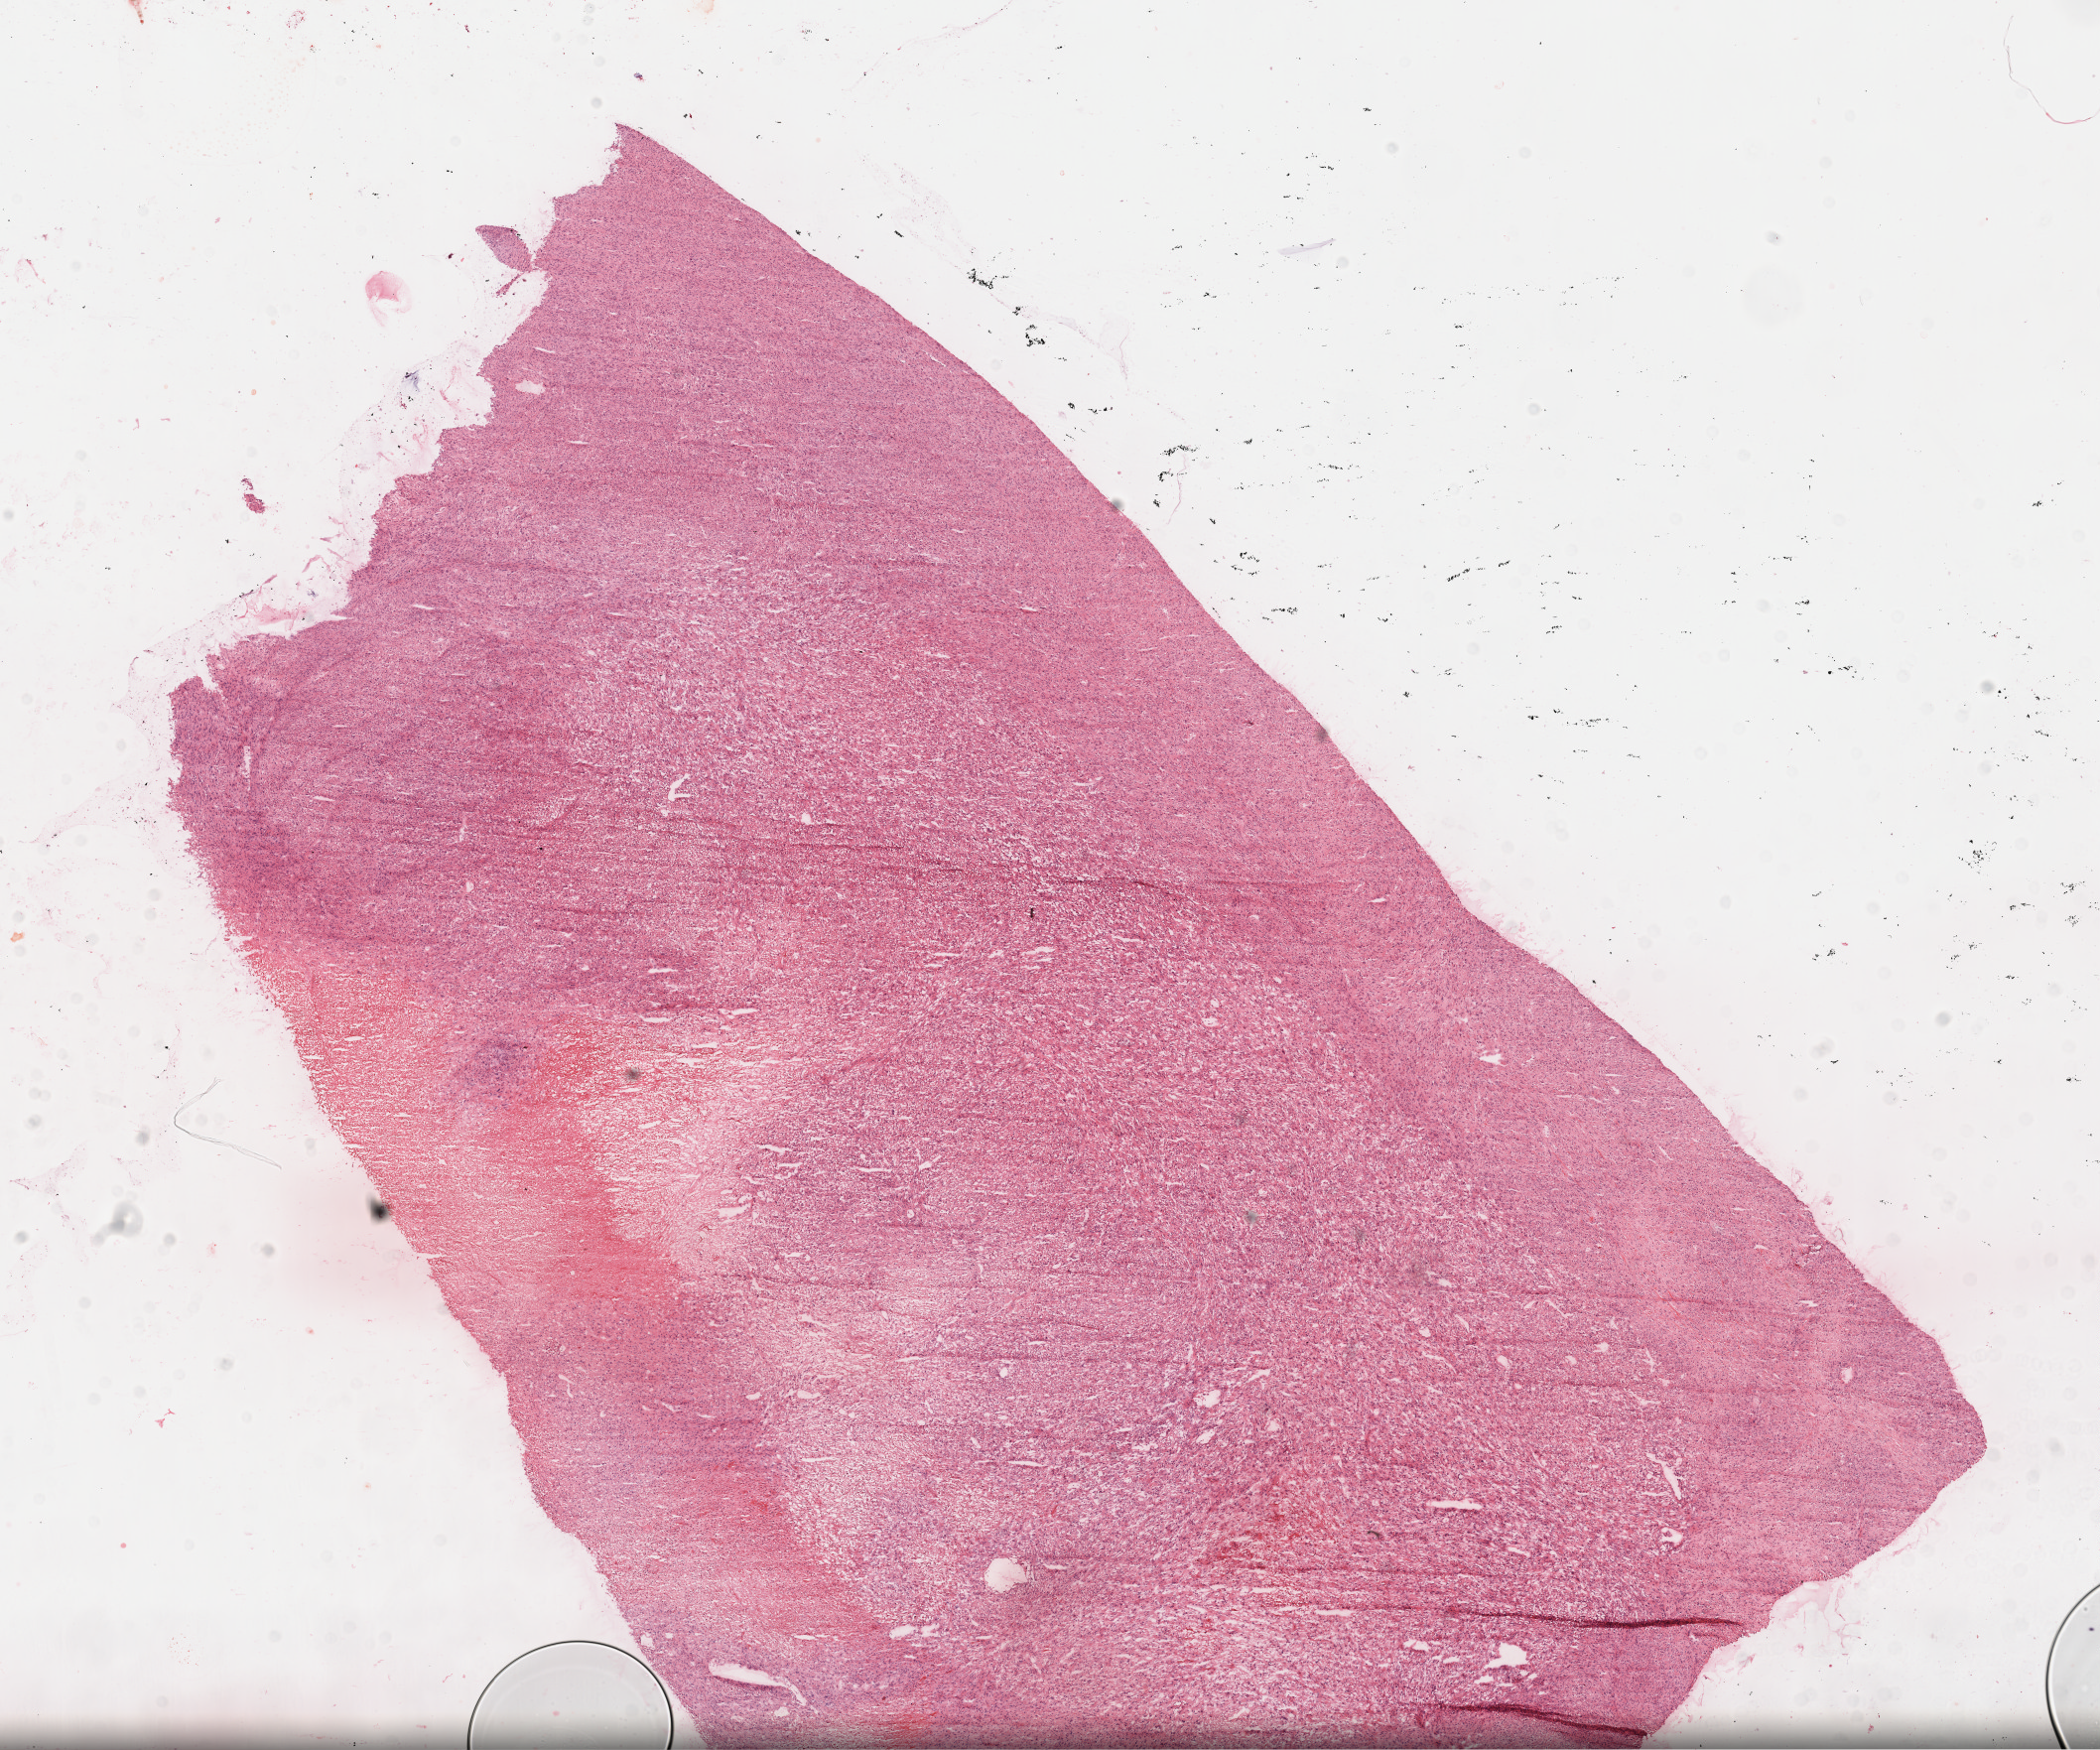
Digitized H&E tissue section (whole slide) — whole scanned area (about 17.1 x 14.3 mm) shown as a low-resolution overview, frozen section from the top of the tissue portion, sample: primary tumour, kidney. Male, age 46 years at initial diagnosis. Histologic grade: G4 (undifferentiated). Slide review estimates, as recorded: tumour cells 65%, tumour nuclei 85%, normal cells 0%, stromal cells 20%, necrosis 15%.
• laterality: left
• diagnosis: Clear cell adenocarcinoma, NOS
• AJCC pathologic stage: IV